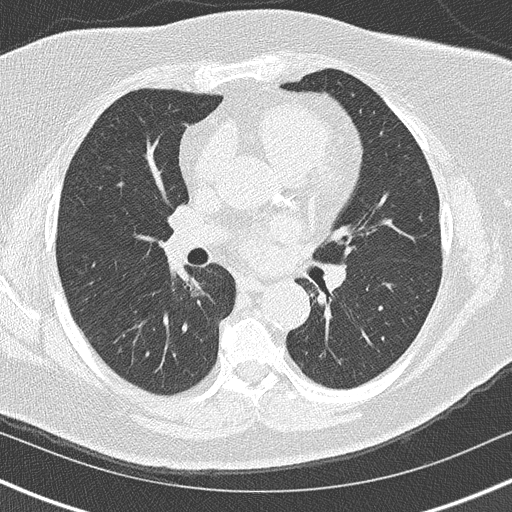
Chest CT (low-dose screening protocol), one axial image, second screening round (one year after baseline), lung window (W 1500 / L -600 HU), 2 mm slice thickness, slice 67 of 152 in the series. Female, age 60 years at enrolment. Former smoker at enrolment.
Expert-annotated lung lesion, bounding box <150,261,211,319> (left, top, right, bottom; pixels). The exam's reader record, not a measurement of the box and not confirmed to be the same lesion: non-calcified nodule or mass ≥4 mm, right lower lobe, 20 × 19 mm, soft tissue attenuation, pre-existing on the prior screen: yes; interval growth: yes. Official screen result: positive, other. Participant outcome: lung cancer diagnosed 139 days after this screen — bronchiolo-alveolar carcinoma, non-mucinous, right lower lobe, stage IA (AJCC 6th edition), 15 mm at pathology.